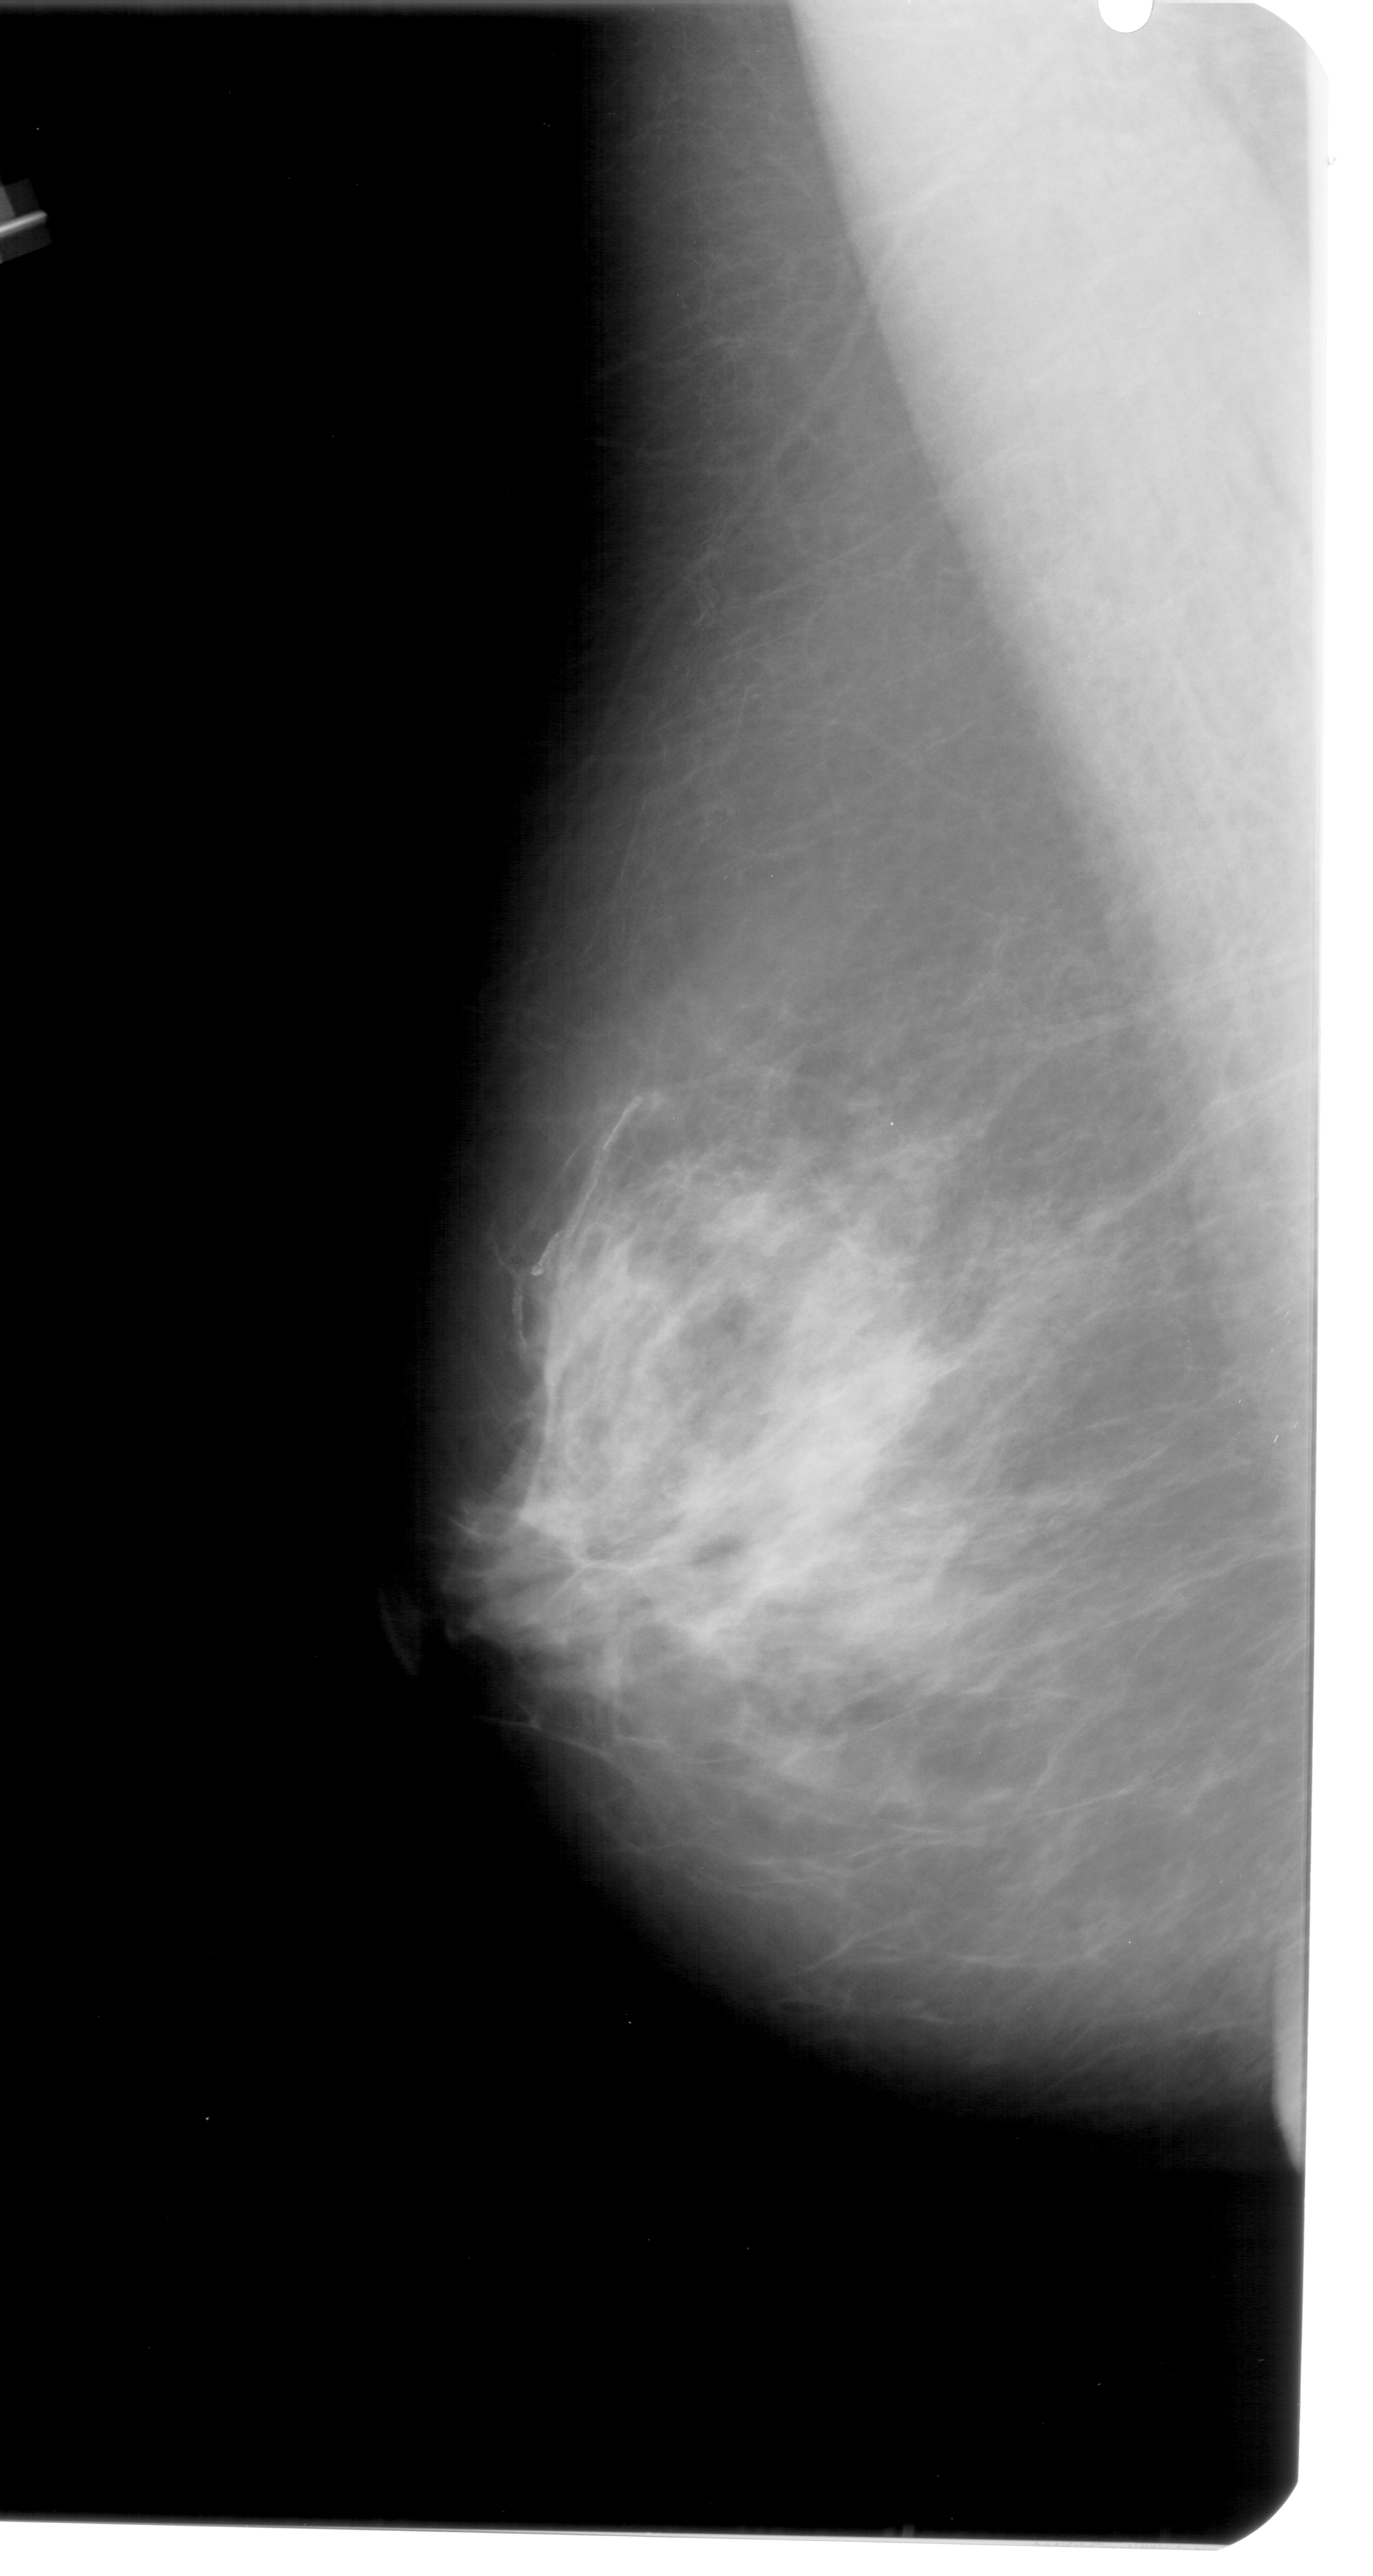
Scanned film-screen mammogram, left breast, mediolateral oblique (MLO) view, breast composition: heterogeneously dense (BI-RADS density category 3 of 4).
Radiologist-marked abnormalities on this image: calcifications, morphology pleomorphic, distribution clustered; BI-RADS assessment category 4; subtlety rating 1 on a 1 (subtle) to 5 (obvious) scale; pathology result (as recorded, not read from the image): benign.